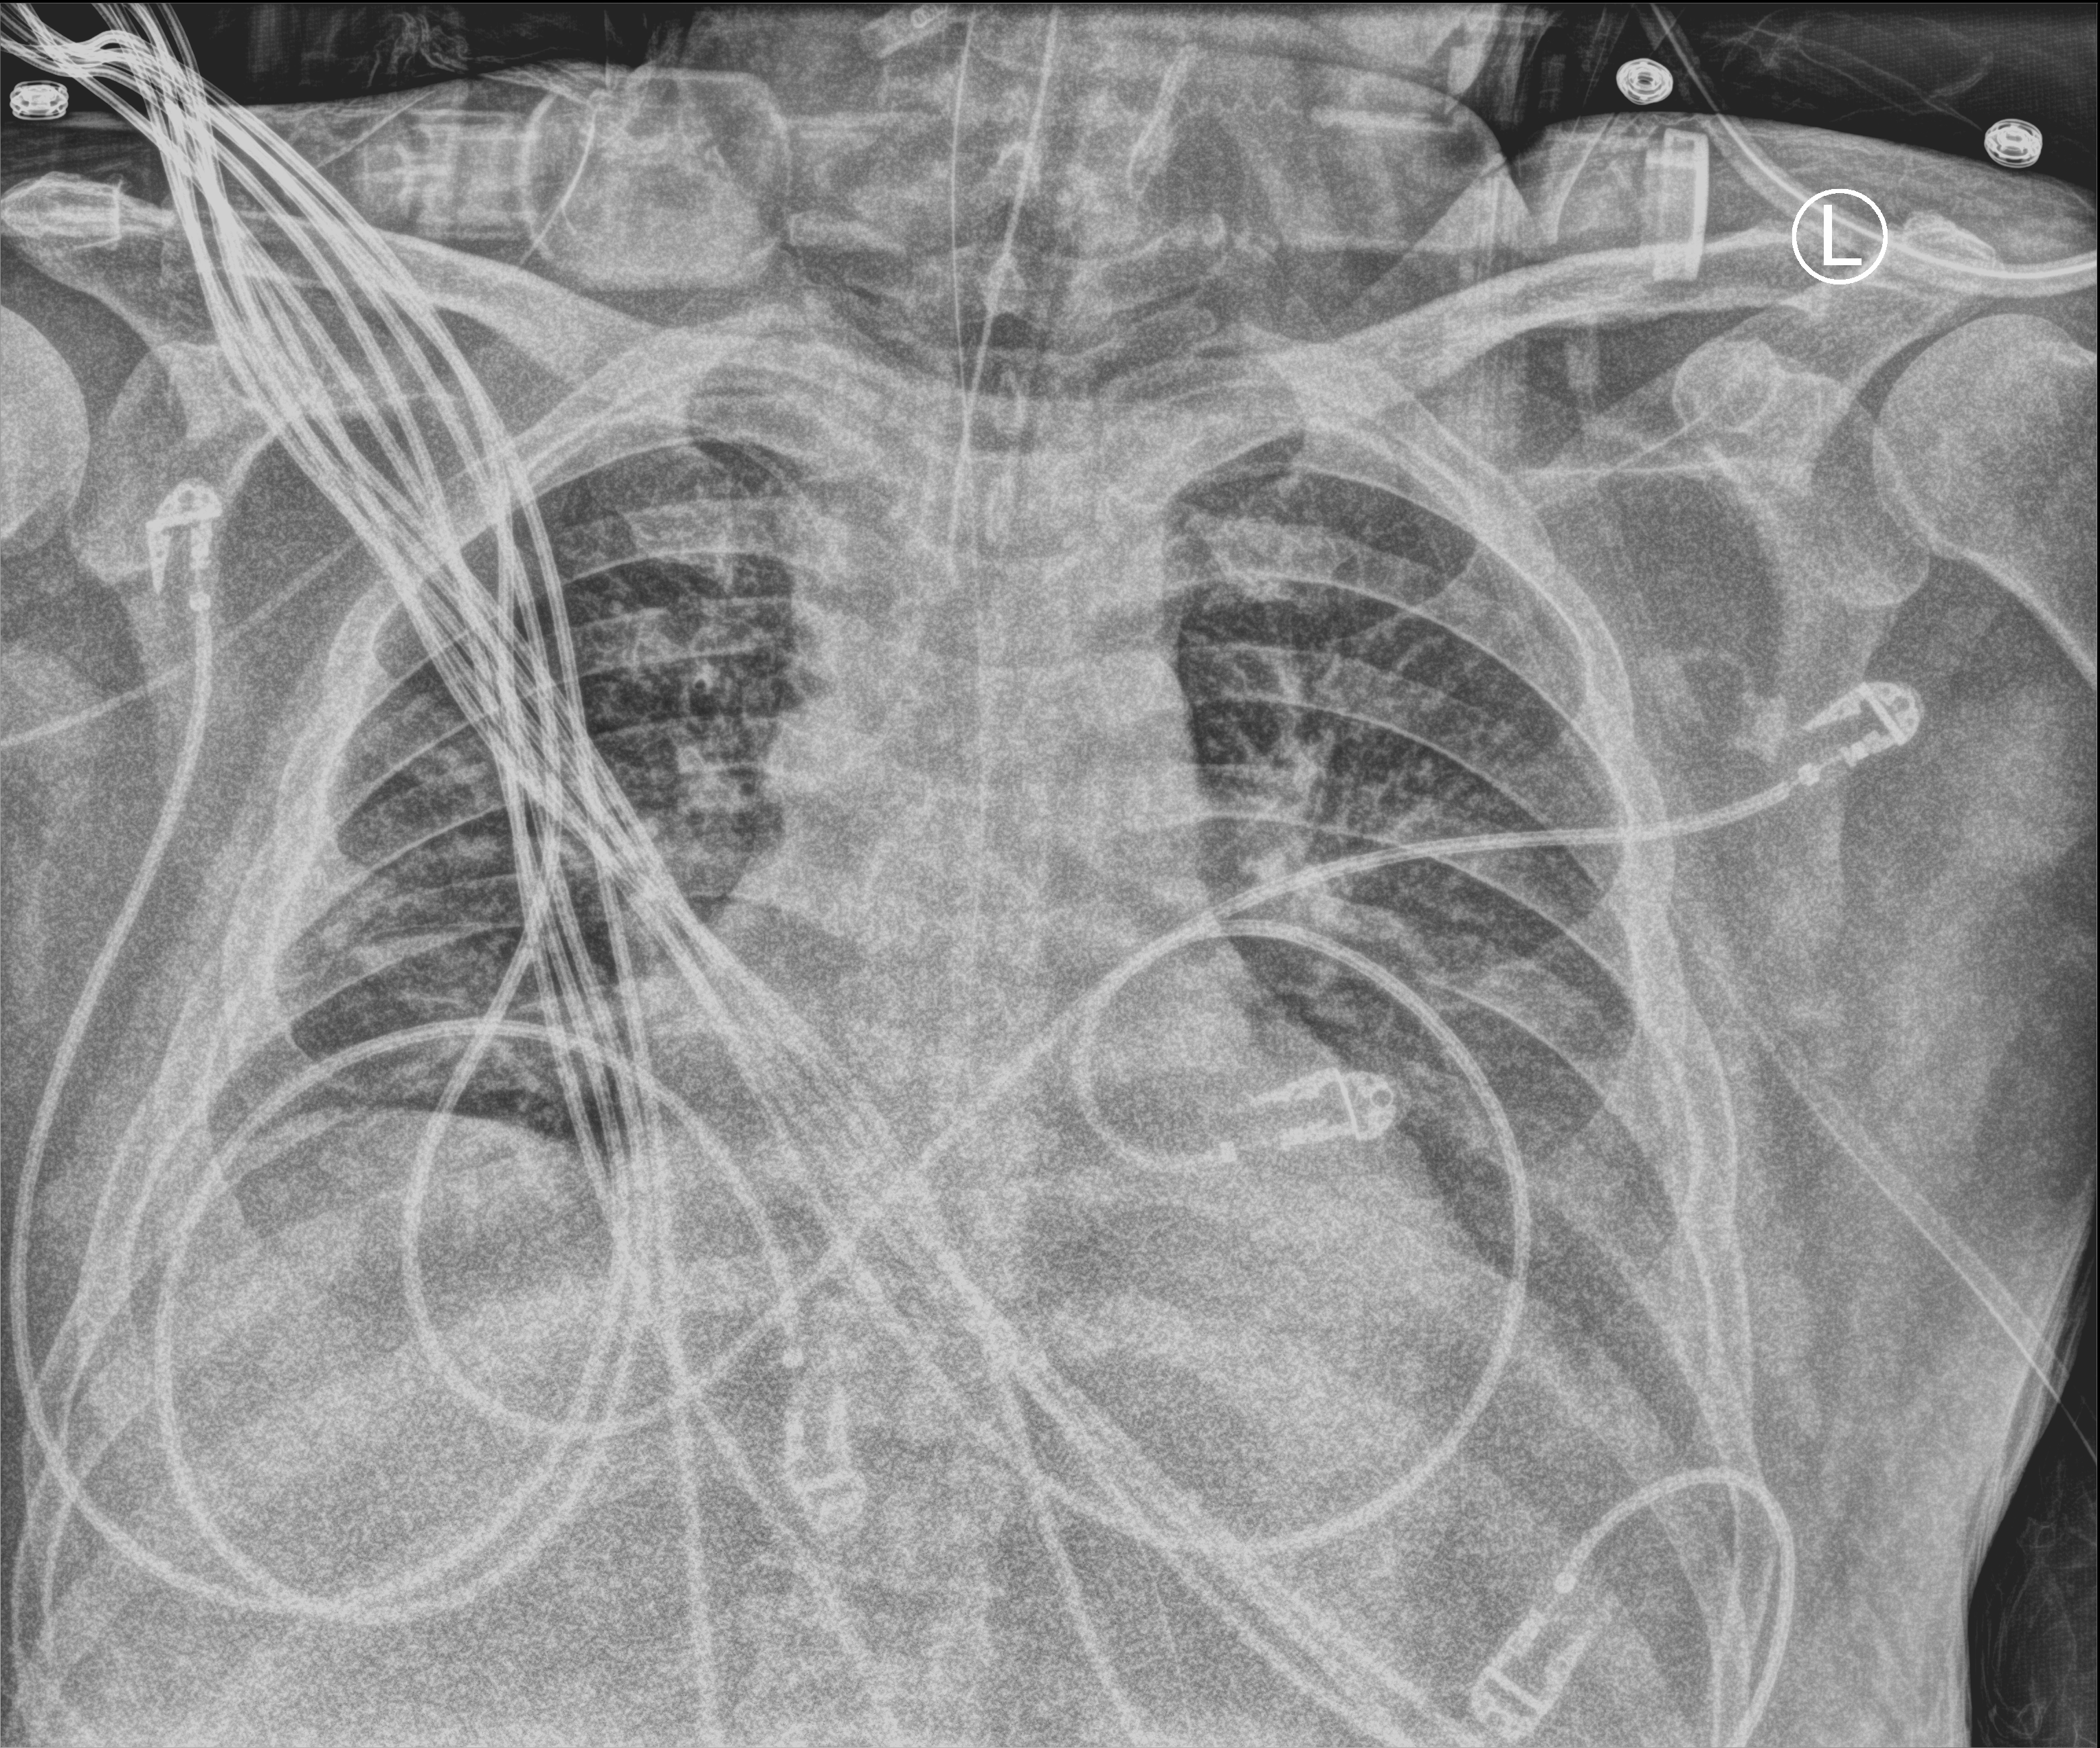
Chest X-ray (portable); anteroposterior (AP) projection. Male patient hospitalised with COVID-19, age 18–59 years.
From the hospital-stay record, not from the radiograph (when in the stay this image was taken is not recorded):
- admitted to intensive care during this hospital stay: yes
- mechanically ventilated during this hospital stay: yes